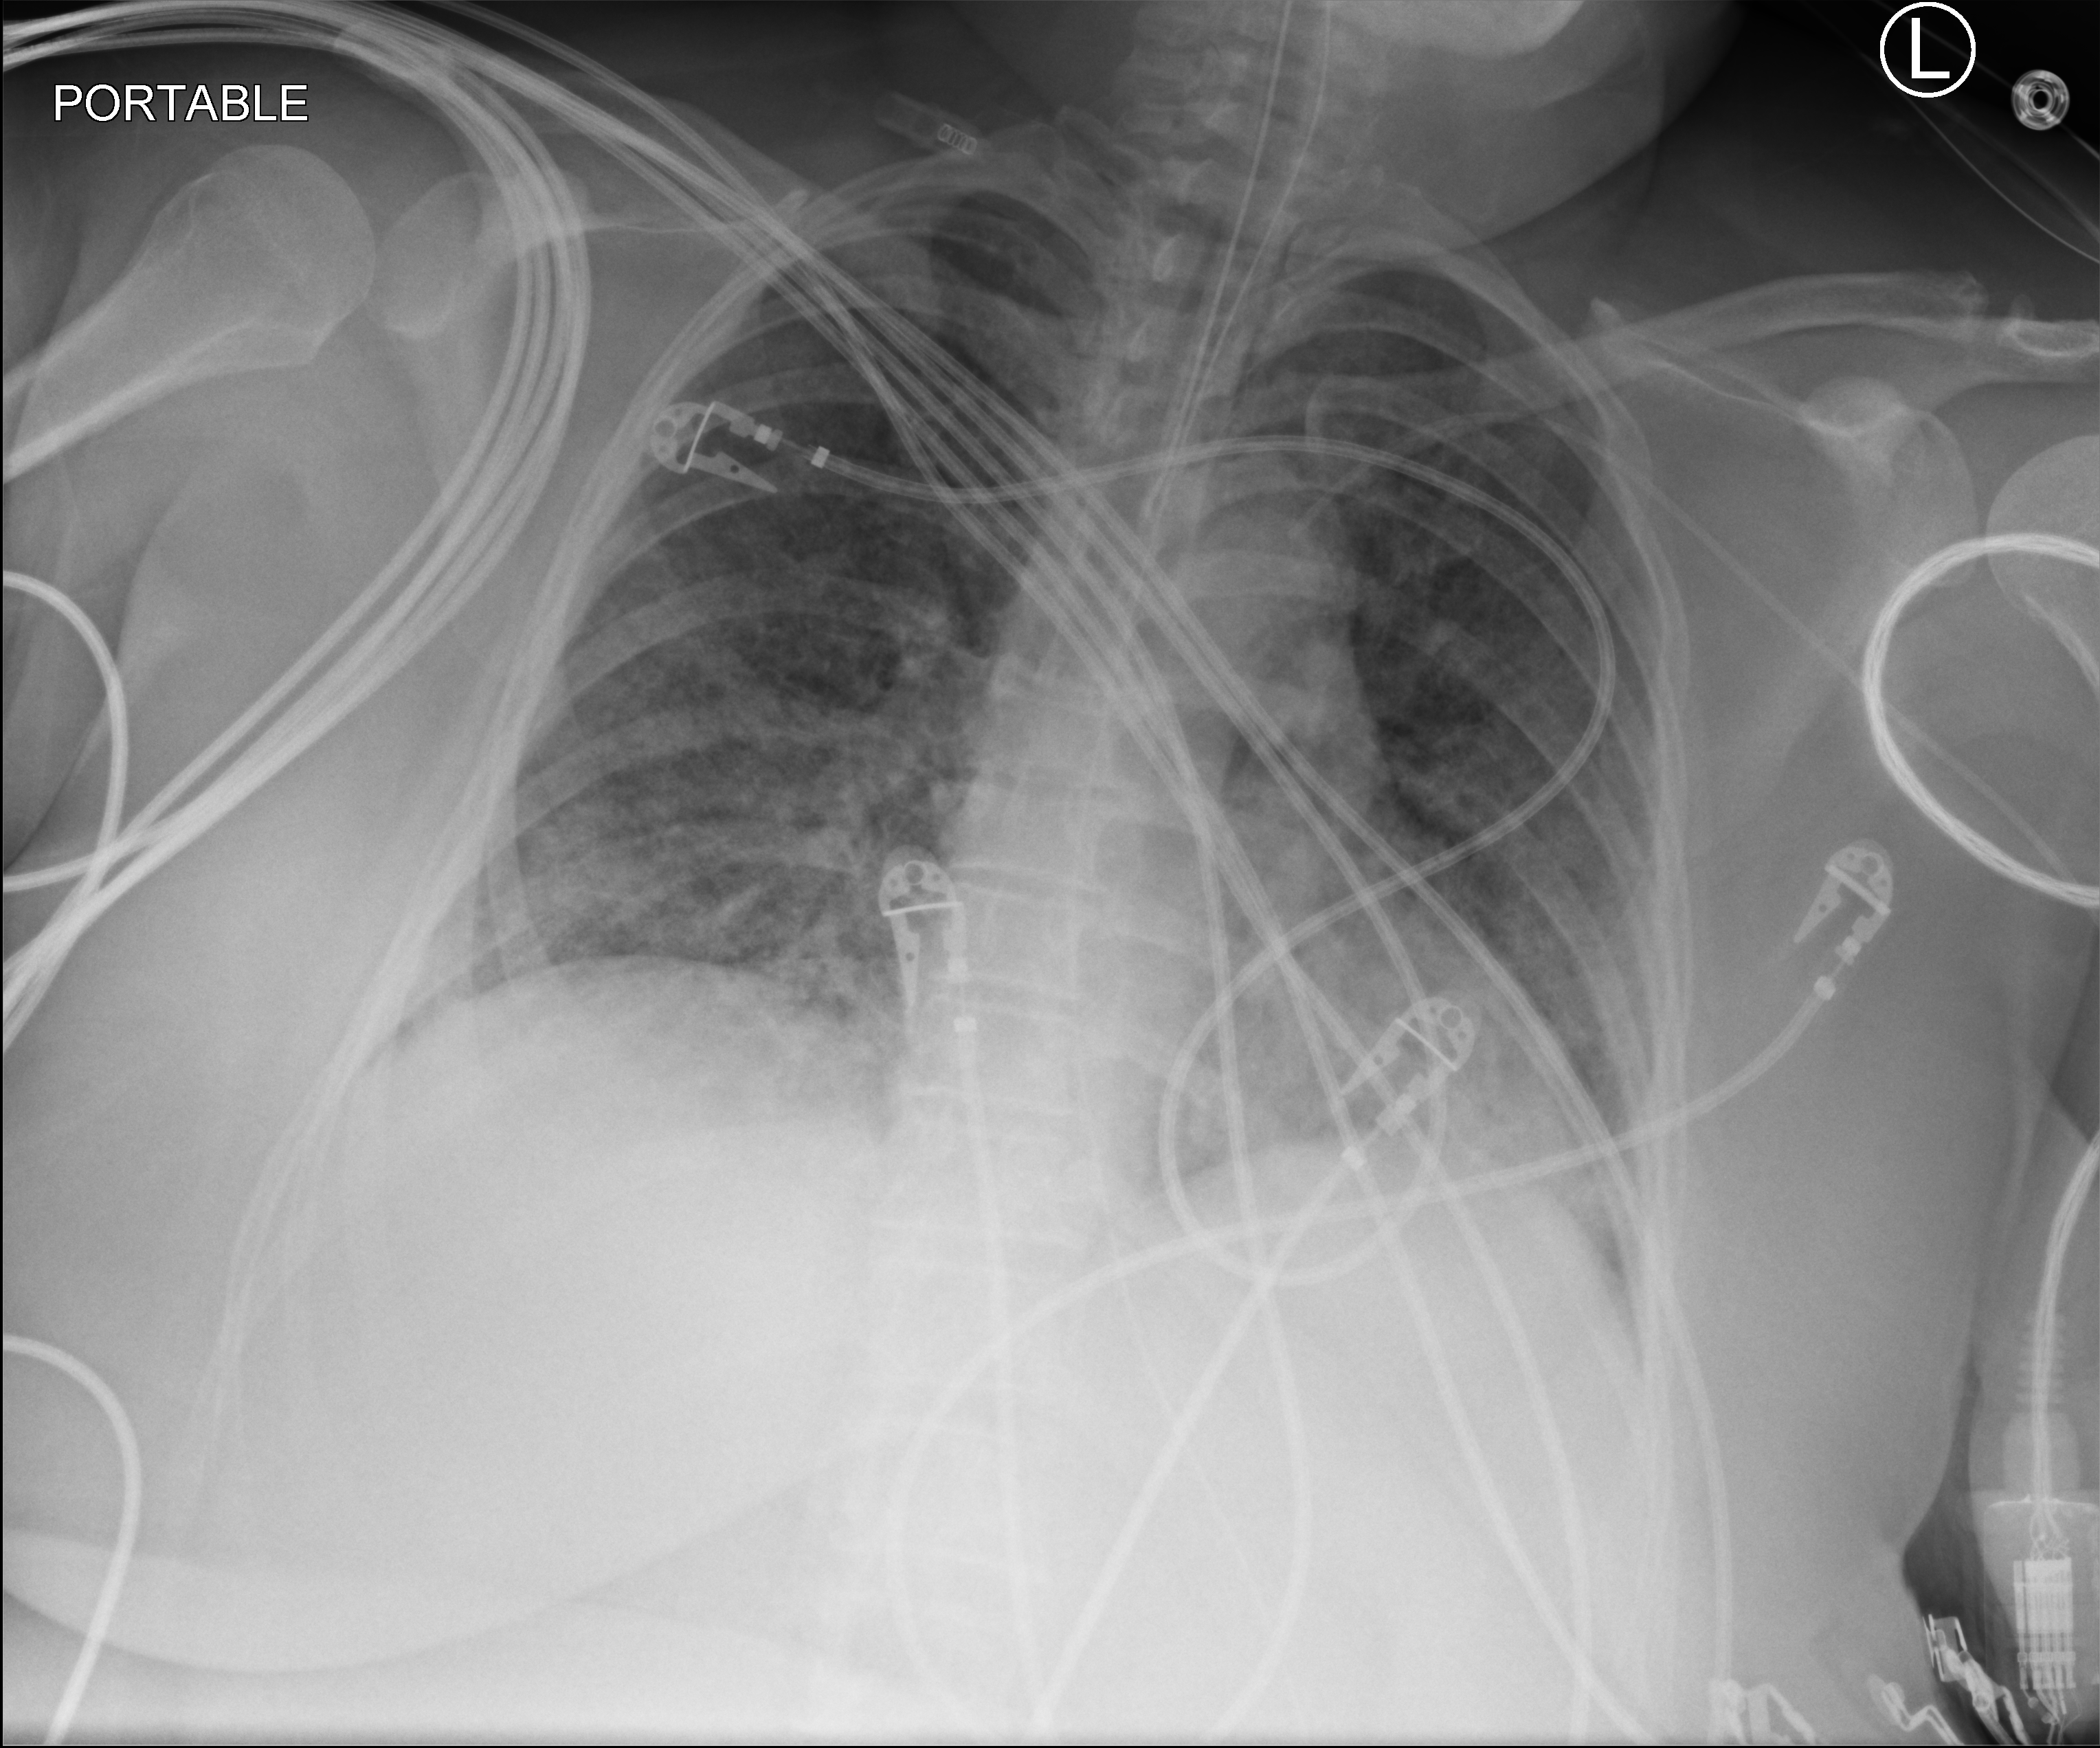
Bedside chest radiograph (computed radiography), anteroposterior (AP) projection. Female patient hospitalised with COVID-19, age 18–59 years.
Admission-level facts for this patient (not findings on this image; timing relative to this image not recorded): length of hospital stay: 95 days; admitted to intensive care during this hospital stay: yes.